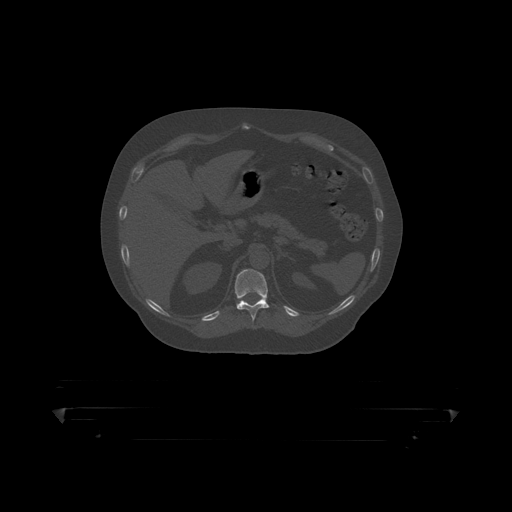
CT including the spine, one axial slice. Slice 193 of 390 in the series (ordered by position). 120 kVp. Bone window (W 1800 / L 400 HU). 1.25 mm slice thickness. 512 × 512 image matrix, field of view 650 × 650 mm. Patient: male, 60 years. From the clinical record (not read from this slice): primary cancer: prostate.
Outlined on this slice (semi-automatic segmentation, software-assisted and operator-edited):
- T11 vertebra: bounding box <235,269,290,319> (left, top, right, bottom; pixels)